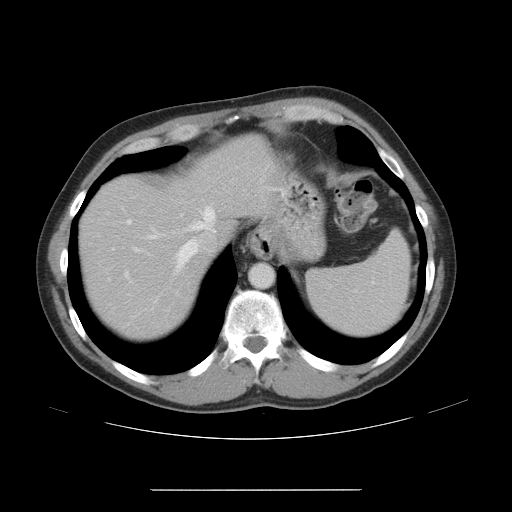
Contrast-enhanced abdominal CT, one axial slice. Position 37 of 48 along the scan axis. 120 kVp. Soft-tissue window (W 400 / L 40 HU). 512 × 512 image matrix, field of view 409 × 409 mm. Male patient, age 56 years. Case-level facts recorded for this patient, not image findings: diagnosis: colorectal cancer liver metastases, imaged before liver resection; multiple liver metastases: yes; largest metastasis: 1.8 cm; disease in both lobes: yes.
Annotated regions visible in this slice (outlined manually by an expert reader):
- hepatic veins: bounding box [x1, y1, x2, y2] px = [147, 207, 216, 302]
- liver: [81, 148, 261, 335]
- planned liver remnant (the part of the liver to remain after resection): [81, 148, 262, 335]
- portal vein (with intrahepatic branches): [126, 219, 140, 252]